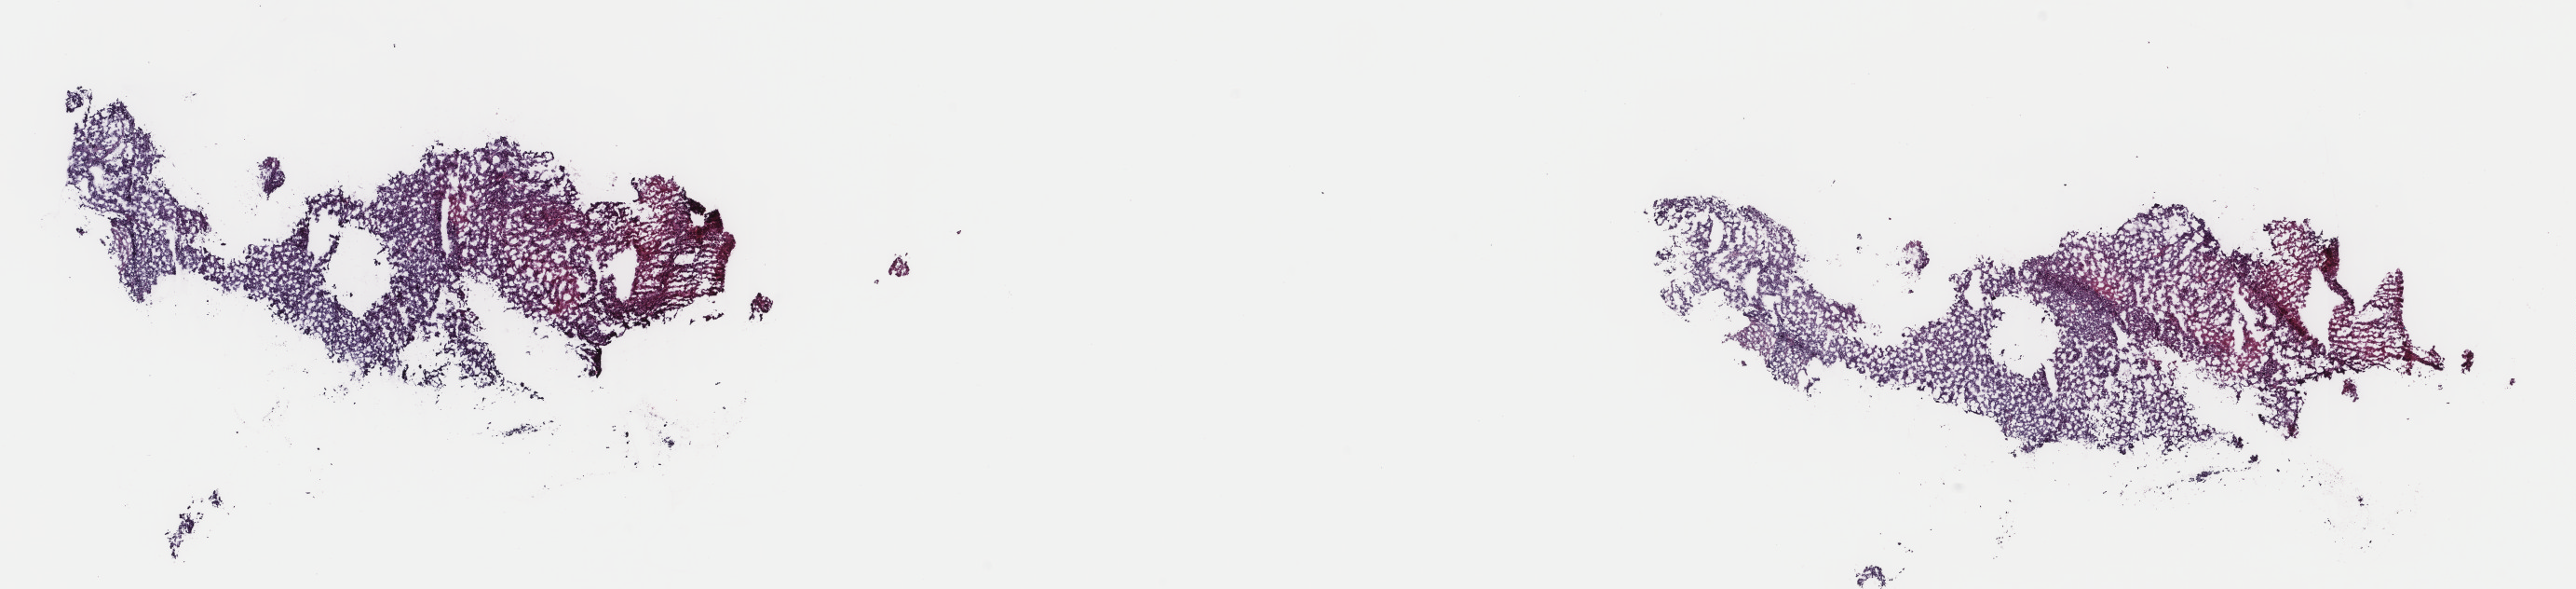
H&E whole-slide image — low-resolution overview of the scanned area, about 22.0 x 5.0 mm (slide scanned at 40x); frozen section from the top of the tissue portion; sample: primary tumour, adrenal cortex. Patient: male, age at initial diagnosis 42 years. Composition of this section per pathologist review: tumour cells 81%, tumour nuclei 80%, normal cells 0%, stromal cells 0%, necrosis 19%. Infiltration values recorded for this section: lymphocyte infiltration 1%, monocyte infiltration 0%, neutrophil infiltration 0%.
Laterality: left. Diagnosis: Adrenal cortical carcinoma (cortex of adrenal gland).